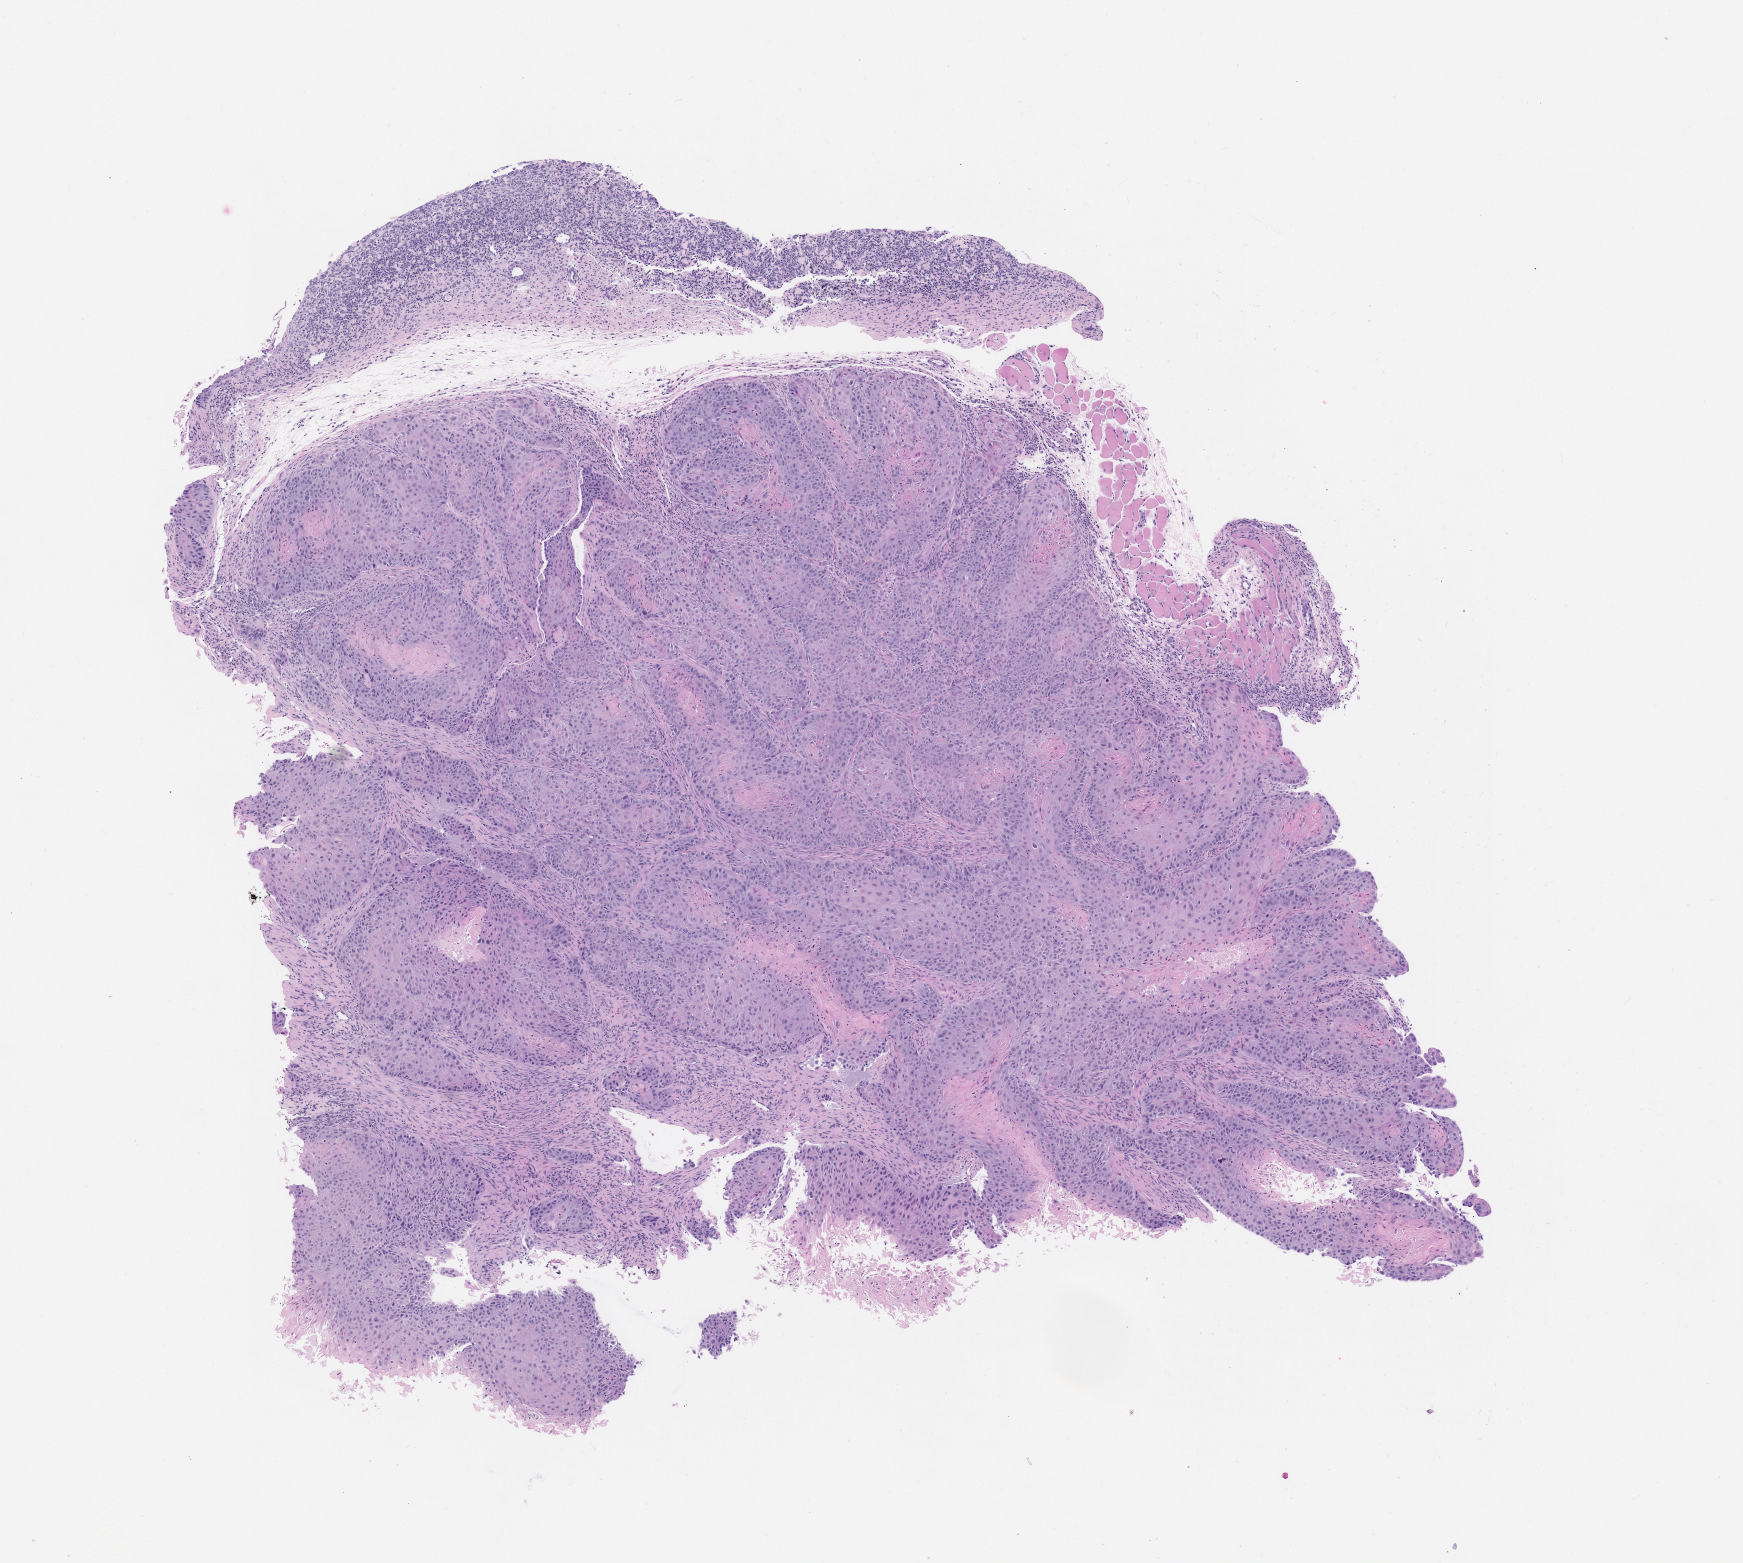
Hematoxylin and eosin (H&E) whole-slide image of a patient-derived xenograft (PDX) tumor grown in a mouse, passage 3 — a low-resolution overview of the entire scanned area, about 7.0 x 6.3 mm; formalin-fixed, paraffin-embedded (FFPE) tissue; tumor site category: lung.
Originating patient diagnosis: Lung Squamous Cell Carcinoma.